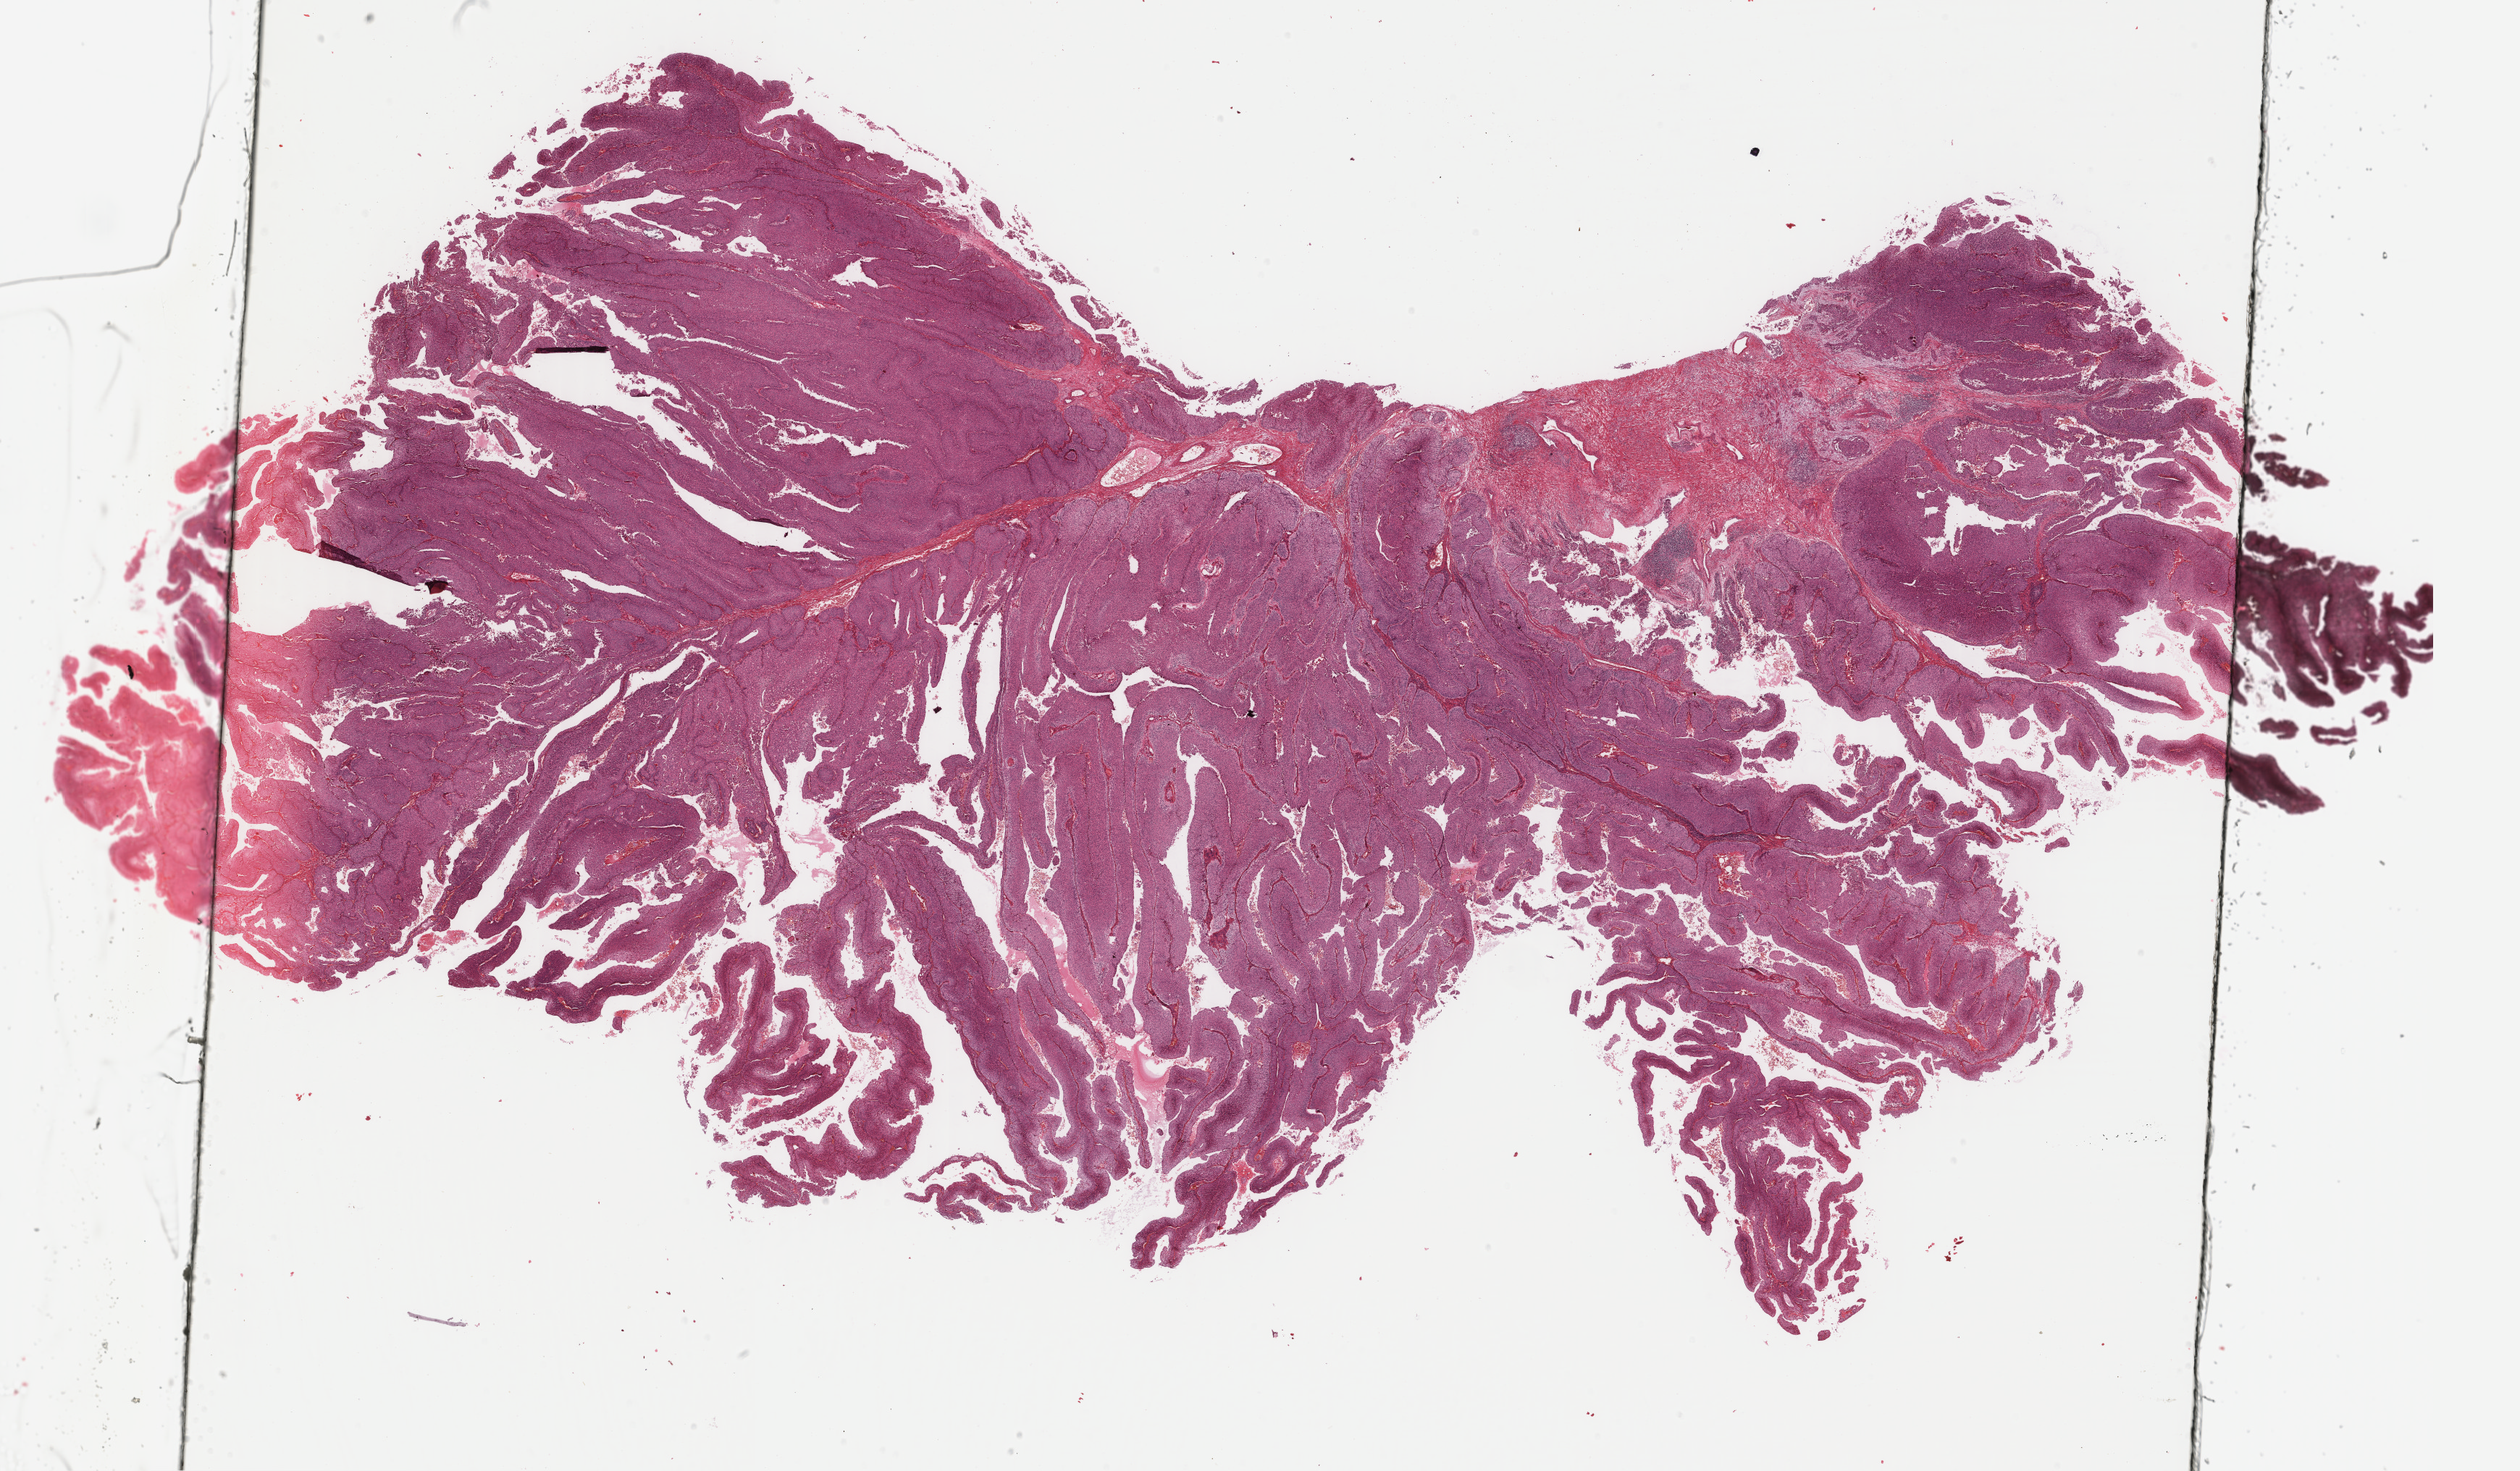
Digitized Hematoxylin and eosin (H&E) stained tissue section (whole slide) — whole scanned area (about 27.6 x 16.1 mm) shown as a low-resolution overview. Formalin-fixed paraffin-embedded (FFPE) diagnostic section. Primary tumour sample from the bladder. Male patient; age at initial diagnosis 52 years. Histologic grade: high grade.
• AJCC pathologic stage: II (7th edition)
• diagnosis: Papillary transitional cell carcinoma